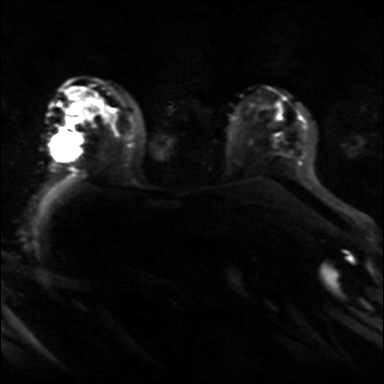
Breast MRI, one axial slice; position 24 of 36 along the scan axis; diffusion-weighted series; image 2 of 4 stored at this slice position (different b-values; order by instance number); 3 T; 384 × 384 image matrix, field of view 320 × 320 mm. Female patient.
Annotated regions visible in this slice (outlined manually by an expert reader):
- tumour on diffusion-weighted imaging: box from (x=48, y=130) to (x=80, y=161) px